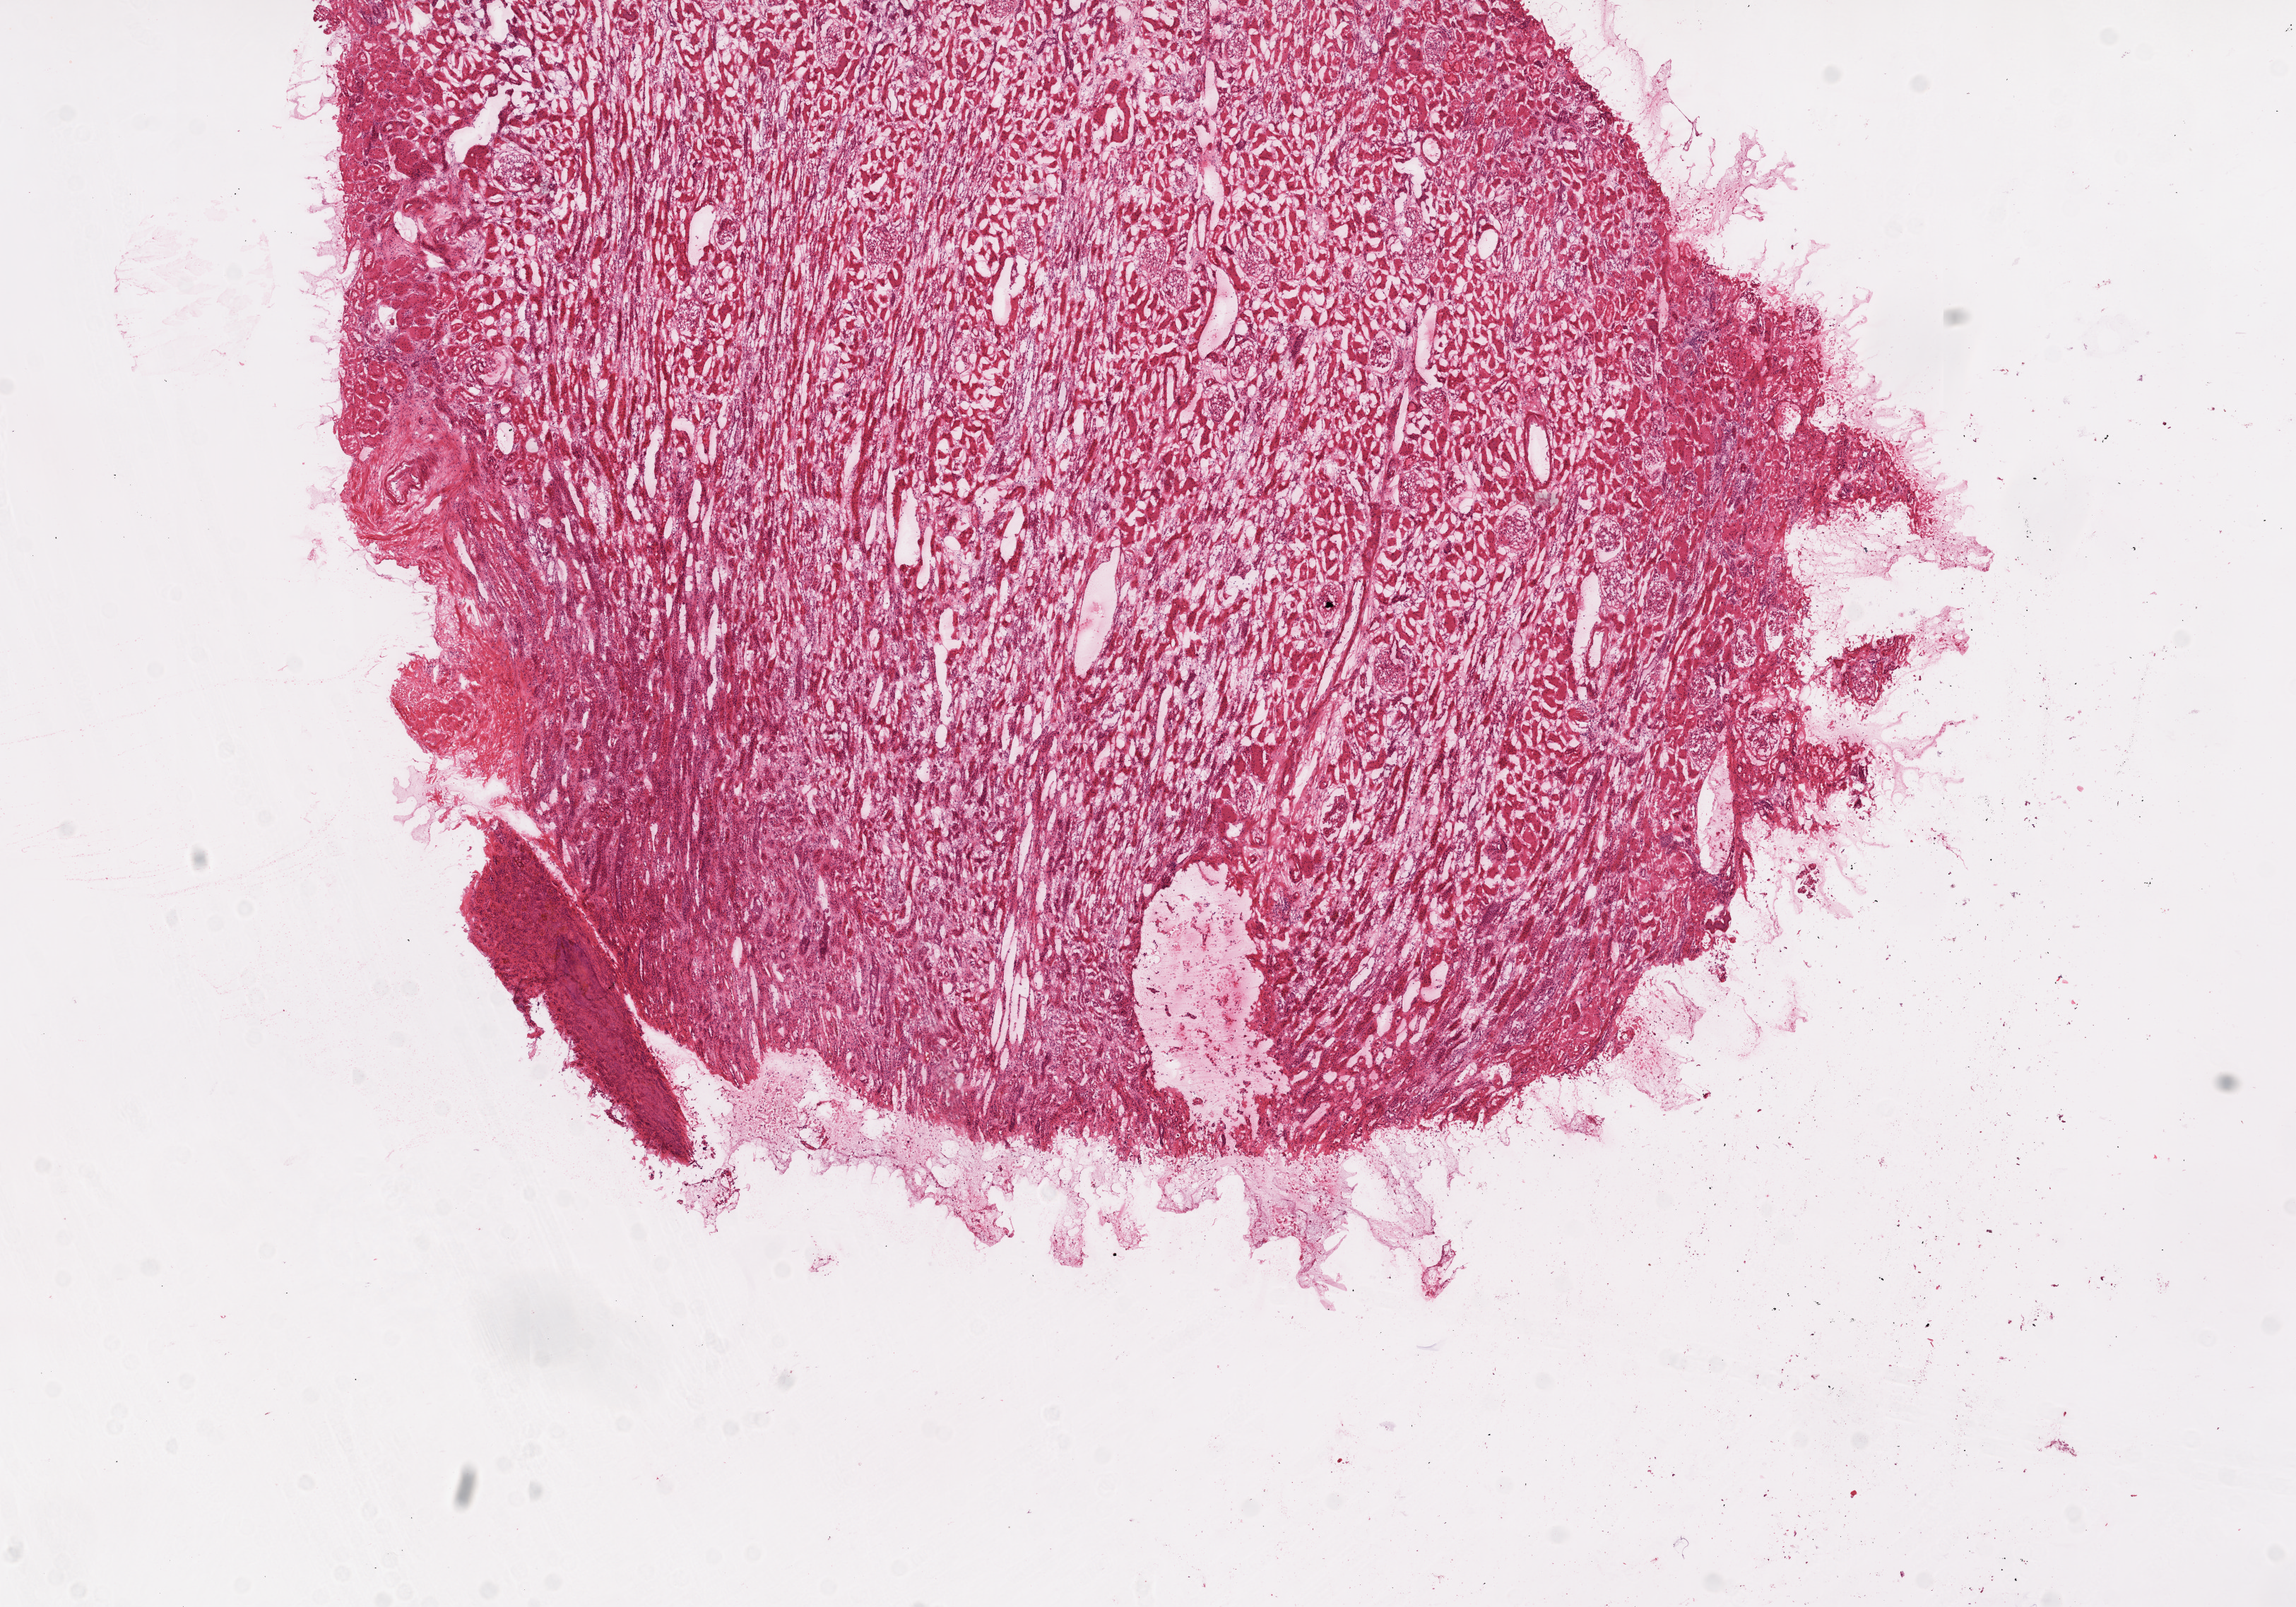
Whole-slide histology image, Hematoxylin and eosin (H&E) stained, a low-resolution overview of the entire scanned area, about 13.0 x 9.1 mm. Frozen section from the top of the tissue portion. Solid tissue normal (non-tumour tissue) sample from the kidney. Patient: female, age at initial diagnosis 69 years.
This section: solid tissue normal (non-tumour) sample from the same patient. Patient diagnosis: Clear cell adenocarcinoma, NOS.